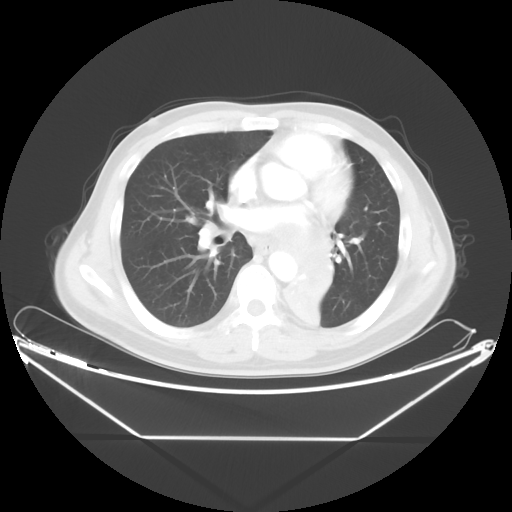
Chest CT, one axial slice; position 22 of 48 along the scan axis; reconstruction kernel STANDARD; lung window (W 1500 / L -600 HU); 5 mm slice thickness; 512 × 512 image matrix, field of view 438 × 438 mm. Patient: male, 58 years. From the clinical record (not read from this slice): clinical TNM (as recorded): T3 N3 M0.
Structures marked on this image (rectangle marked by the reading radiologist):
- lung tumour (recorded histology: squamous cell carcinoma): bounding box (x1, y1, x2, y2) in pixels: (270, 244, 367, 350)